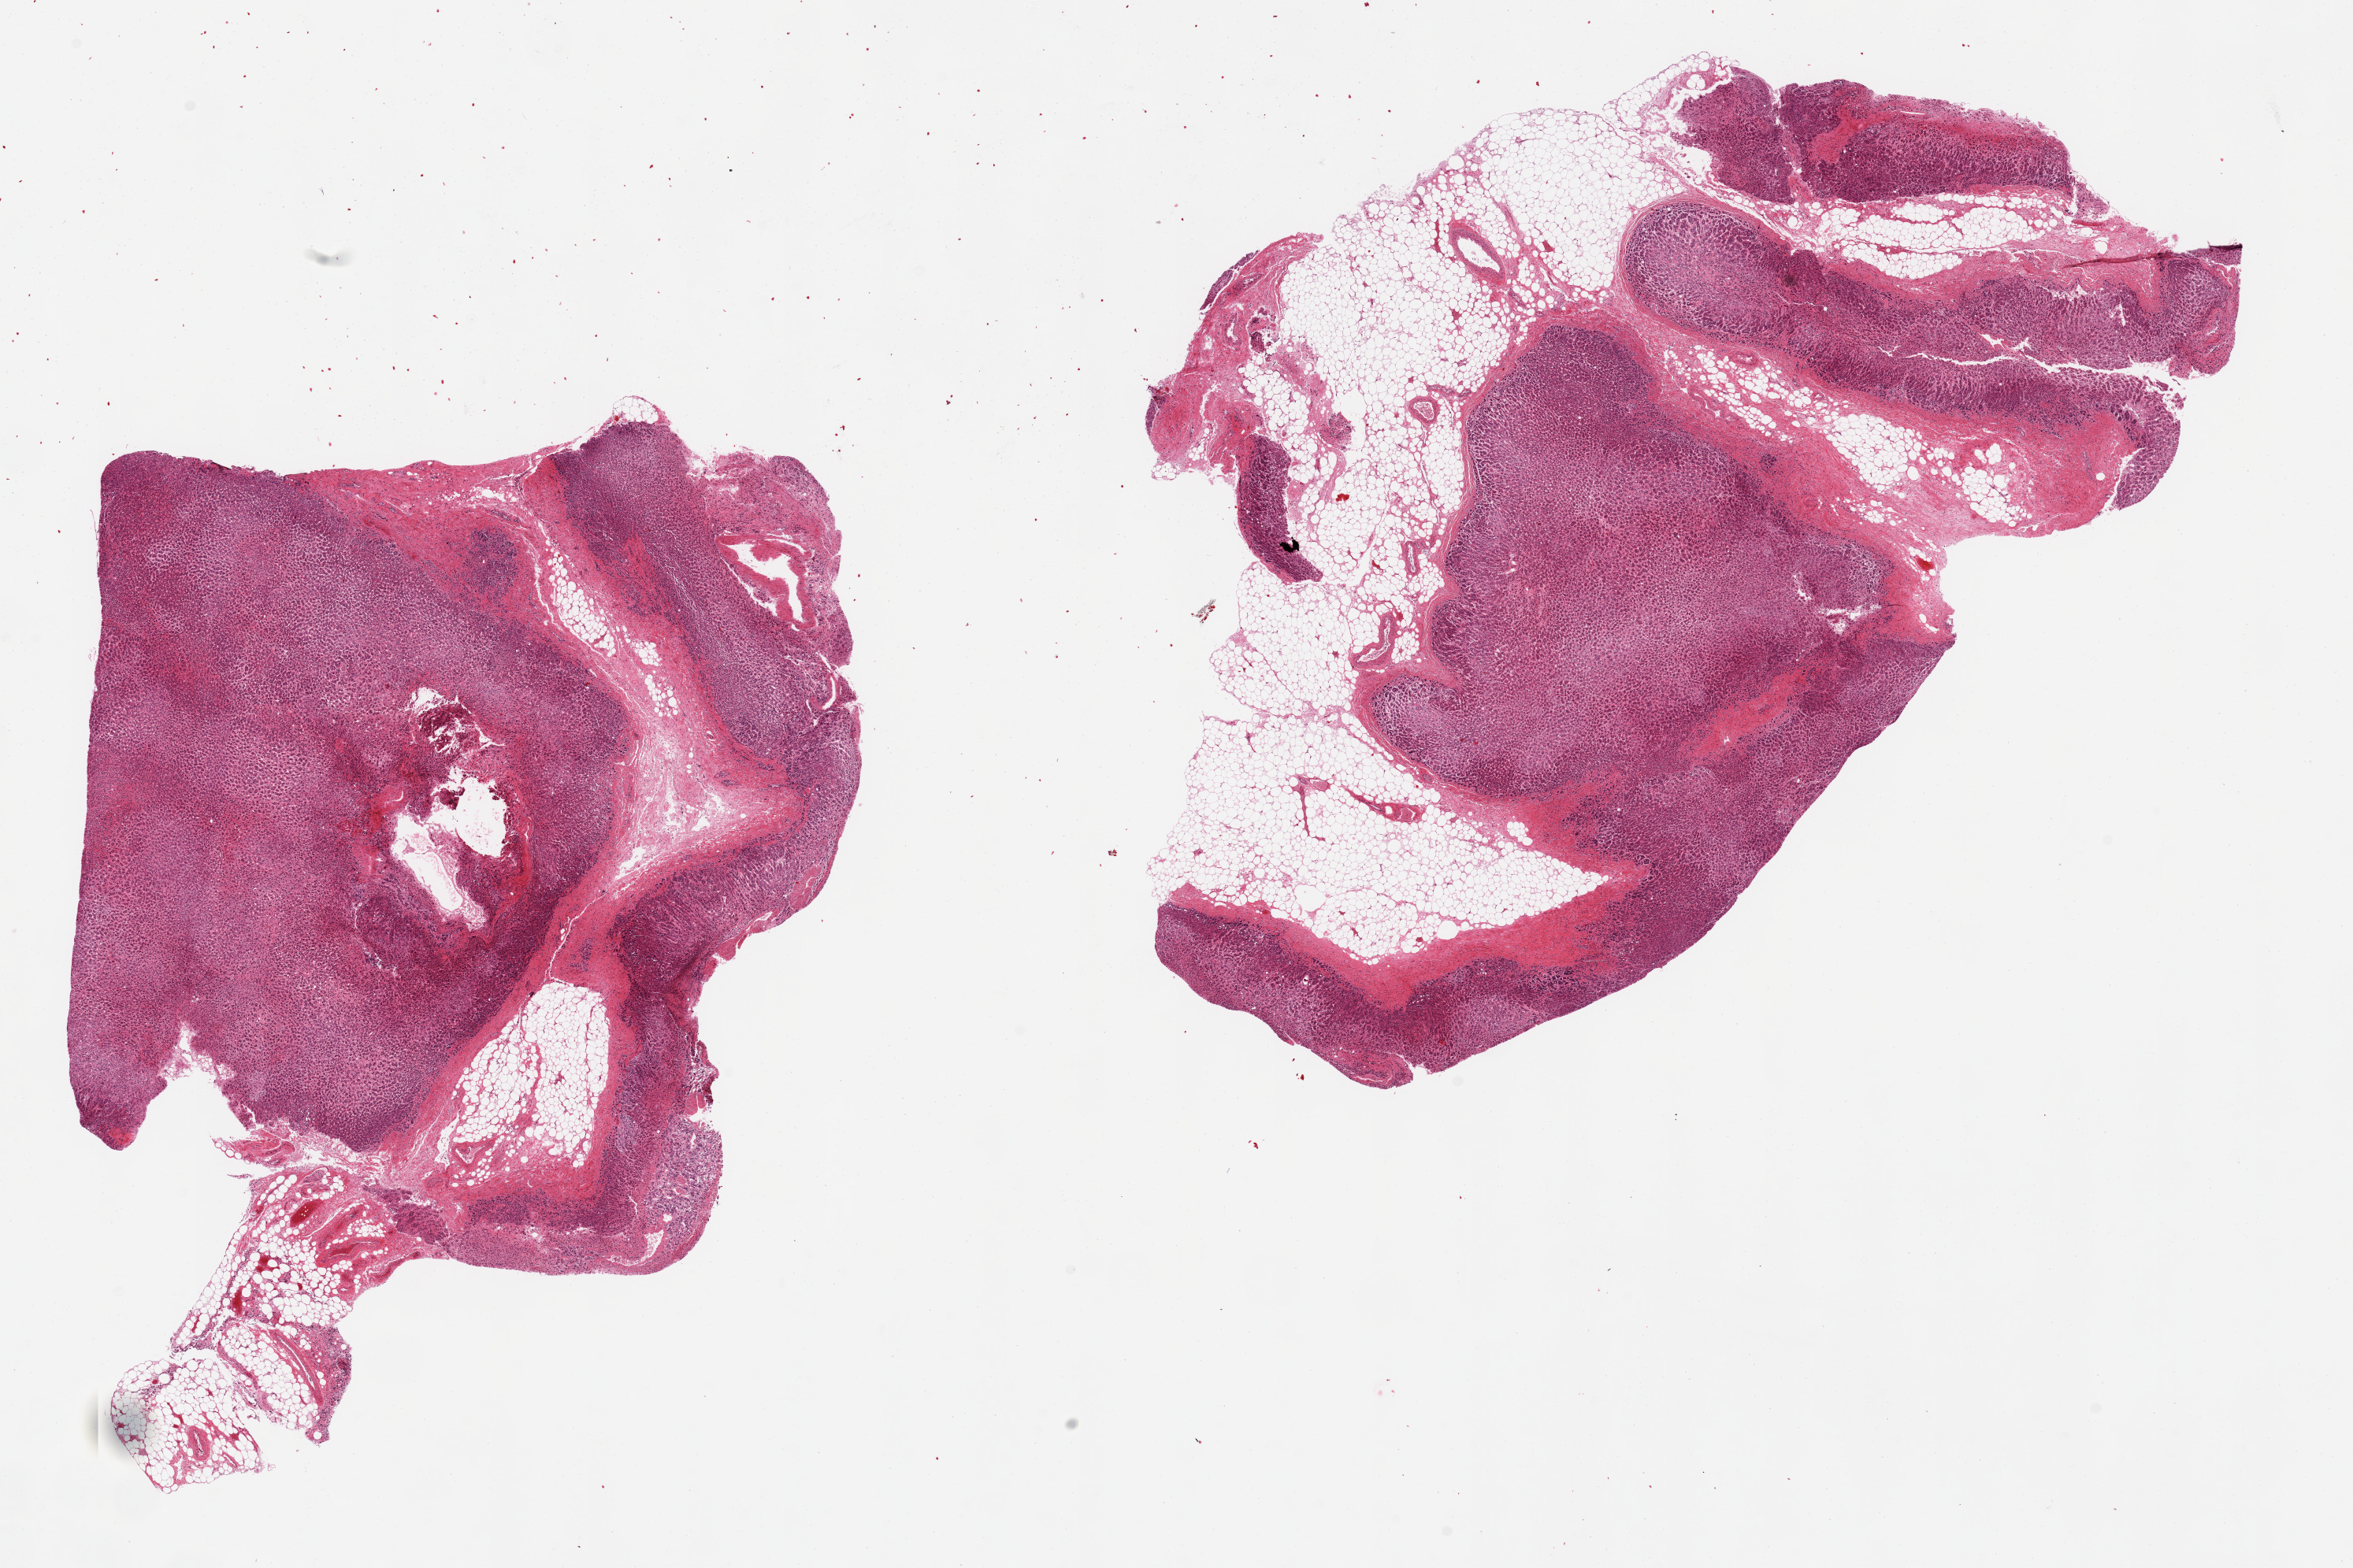
Digitized haematoxylin and eosin-stained section, a low-resolution overview of the entire scanned area, about 23.6 x 15.7 mm (slide scanned at 20x). PAXgene-fixed, paraffin-embedded tissue. Sampled site (target tissue): adrenal gland. Donor tissue sample. Male donor.
Pathologist's review note for this sample: 2 pieces: with 20% and 40%internal and external fat.